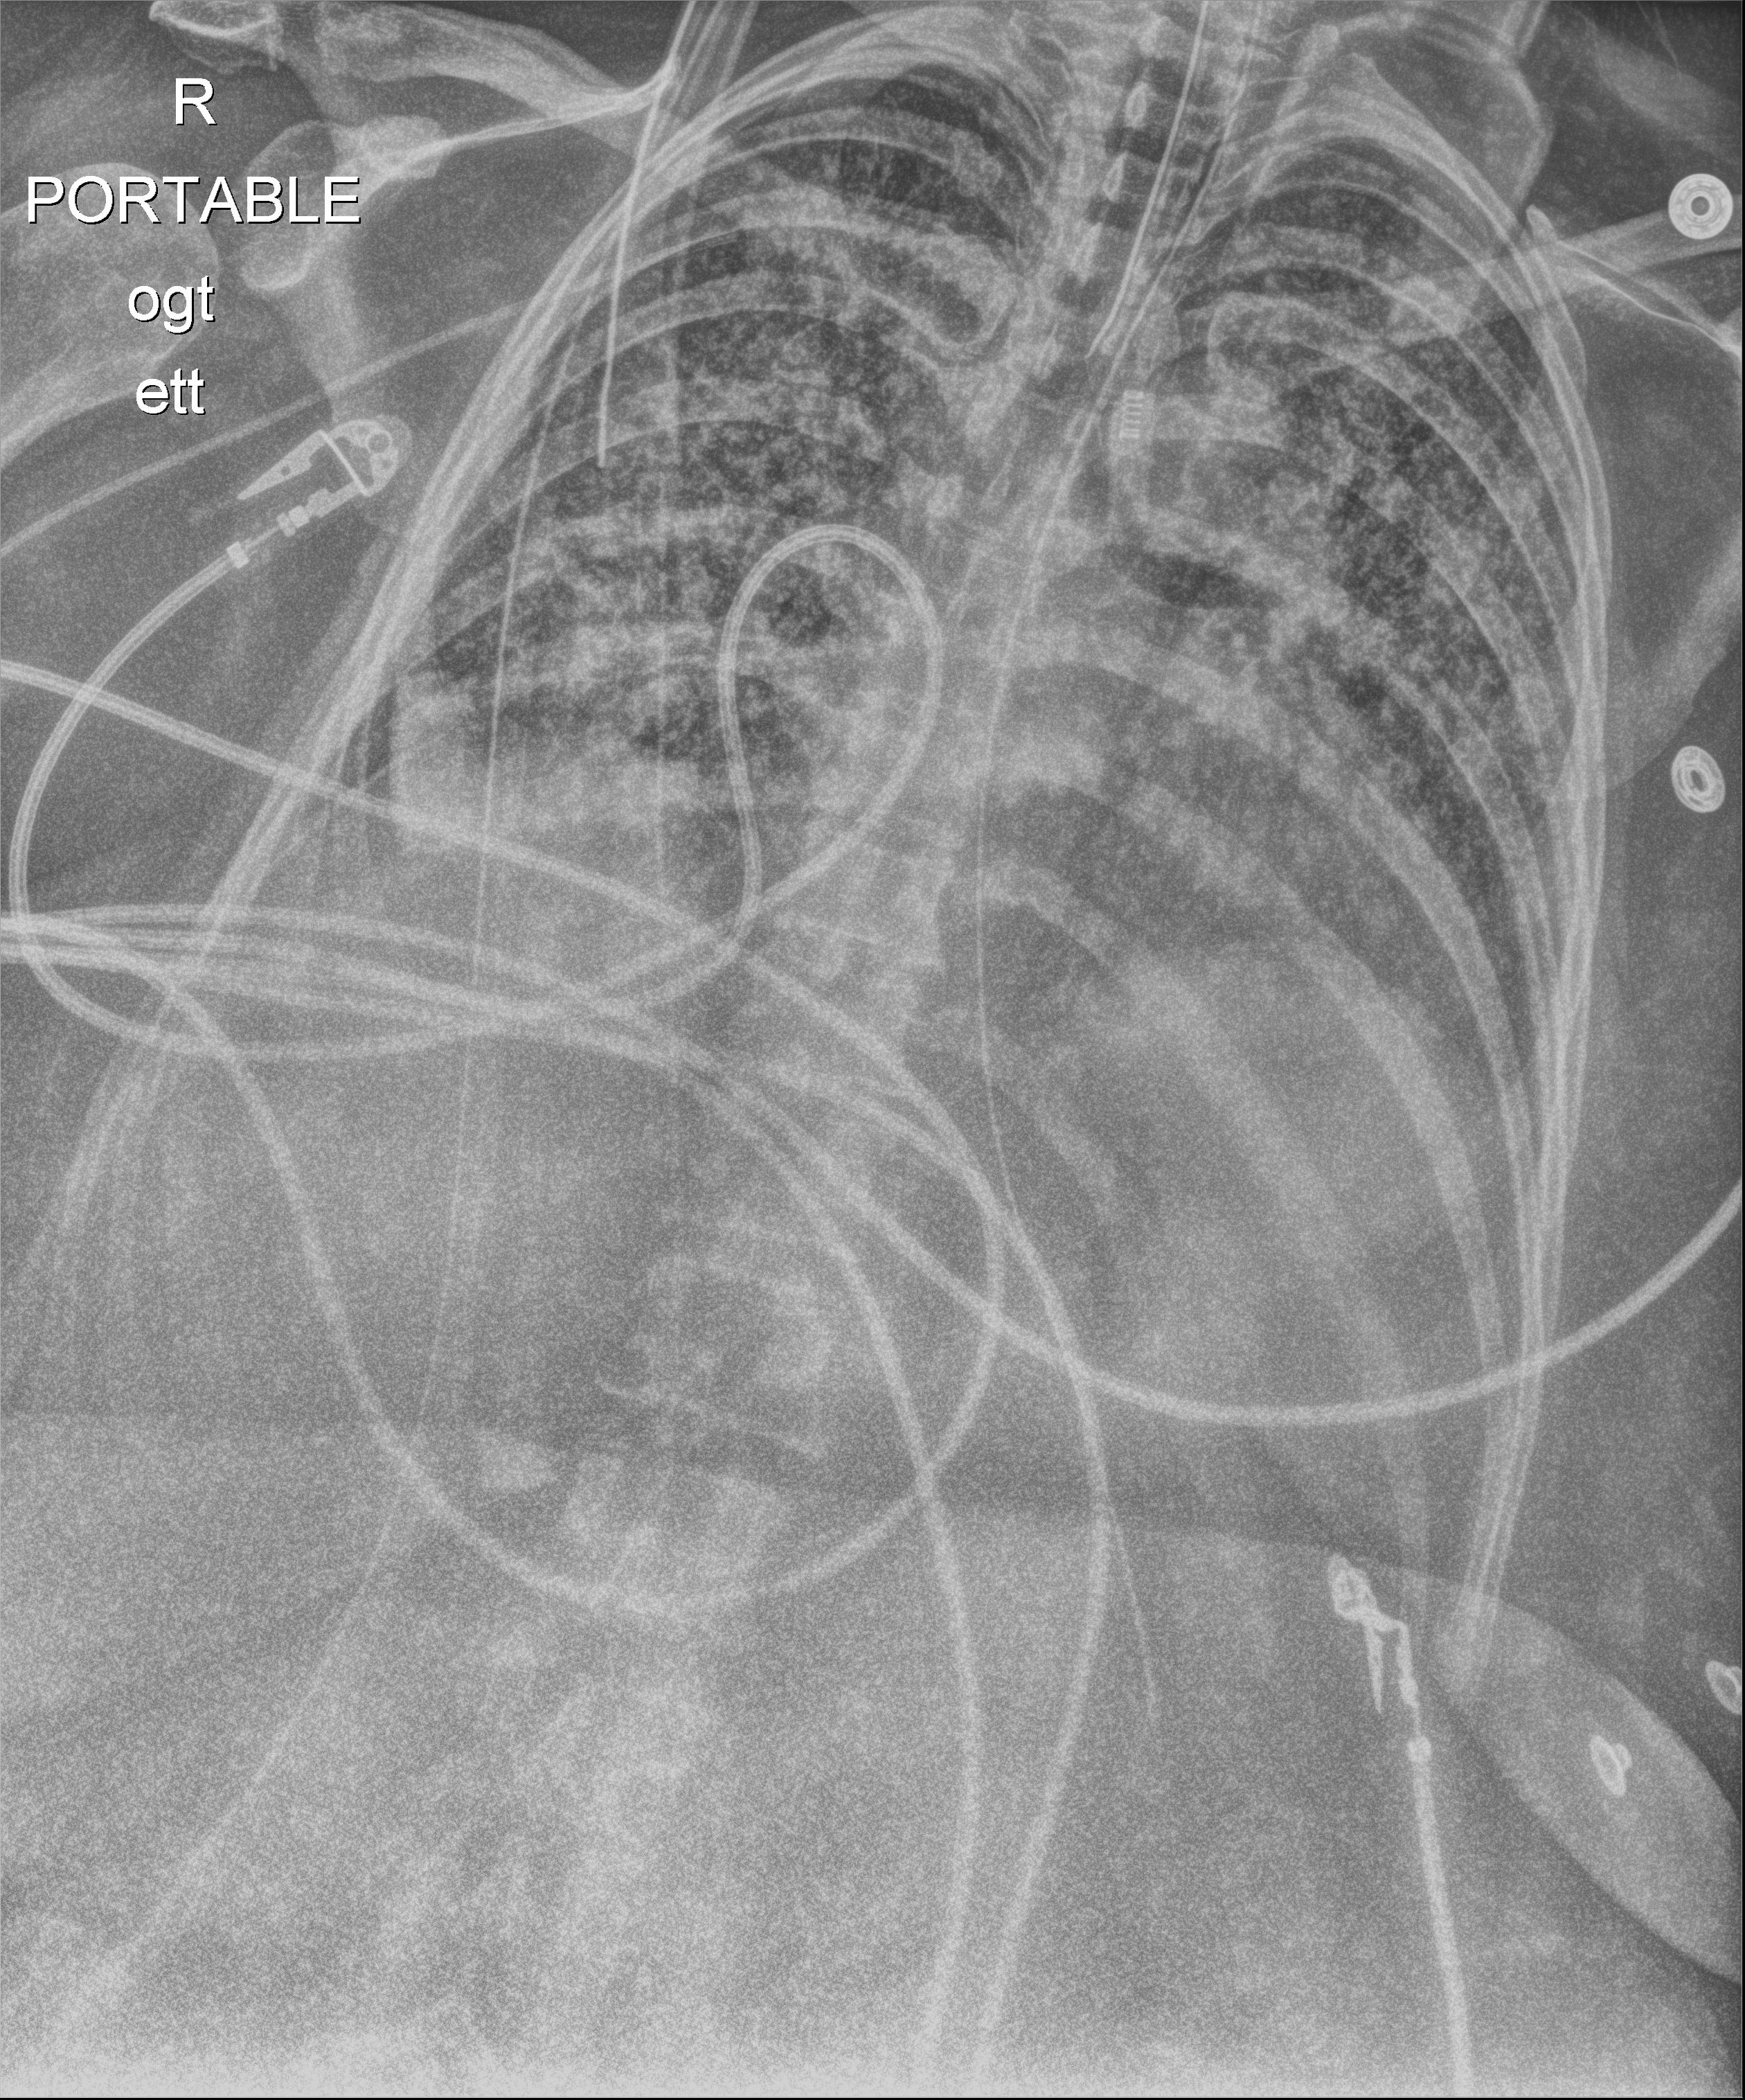
Chest X-ray; anteroposterior (AP) projection. Female patient hospitalised with COVID-19, age 18–59 years.
Hospital-stay facts (about this admission, not read from this image; timing relative to this image not recorded): admitted to intensive care during this hospital stay: yes.